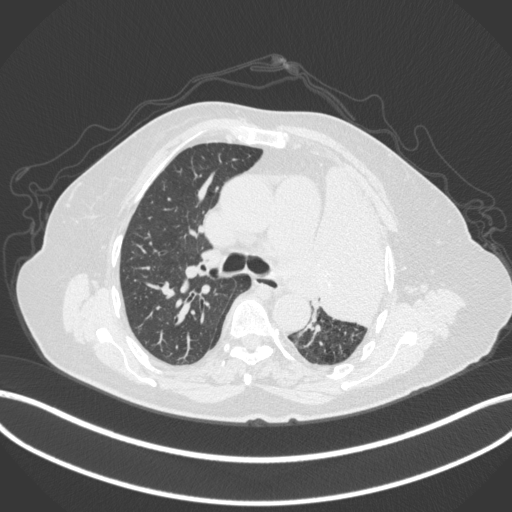
Chest CT, one axial slice. Slice 252 of 399 in the series (ordered by position). 120 kVp. Lung window (W 1500 / L -600 HU). 512 × 512 image matrix, field of view 400 × 400 mm. Female patient, age 75 years. From the clinical record (not read from this slice): clinical TNM (as recorded): T3 N3 M1.
Annotated regions visible in this slice (rectangle marked by the reading radiologist):
- lung tumour (recorded histology: adenocarcinoma): box from (x=315, y=152) to (x=395, y=329) px